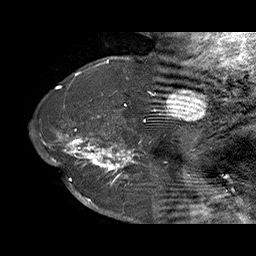
Breast MRI (dynamic contrast-enhanced), one sagittal slice; slice 52 of 70 in the series (ordered by position); dynamic contrast-enhanced series, time point 2 of 6 at this slice position (early post-contrast); 1.5 T; TE 4.5 ms, TR 32.4 ms; 3 mm slice thickness; 256 × 256 image matrix, field of view 180 × 180 mm. Female patient. Case-level facts recorded for this patient, not image findings: setting: breast cancer imaged before/during neoadjuvant chemotherapy; receptor status: HR-positive, HER2-negative.
Outlined on this slice (semi-automatically segmented with operator editing):
- analysis volume of interest (the breast-tissue region the enhancement analysis was run in; not a lesion): box from (x=71, y=128) to (x=159, y=202) px
- tumour enhancement mask (voxels above the 100 % enhancement threshold inside the analysis volume of interest): (x=71, y=128)–(x=145, y=202)